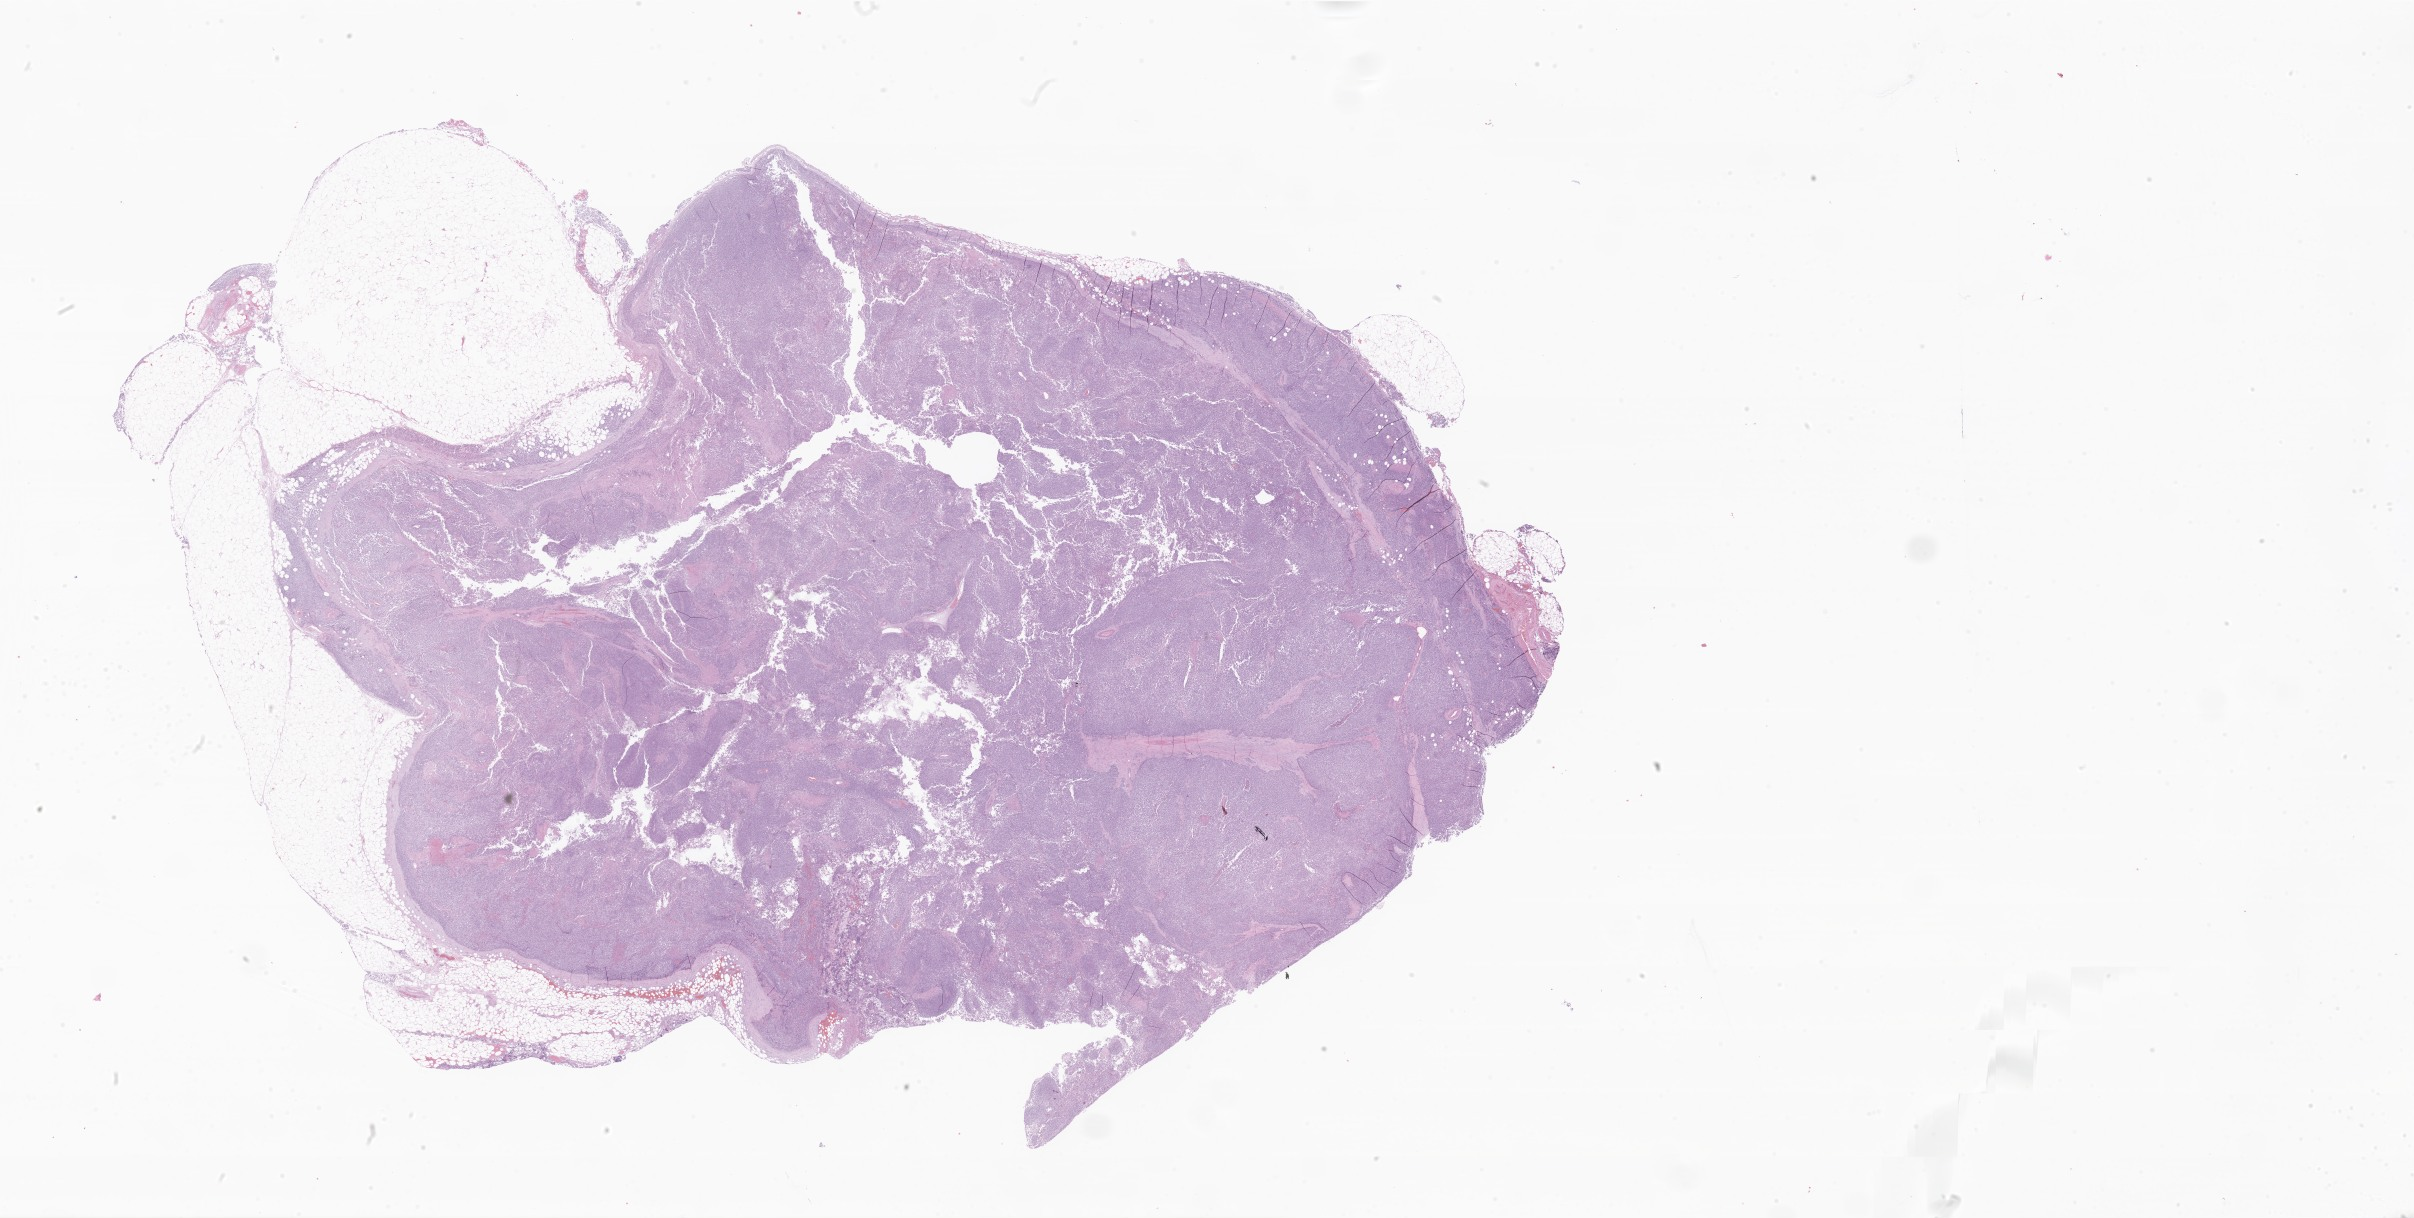
Whole-slide image, H&E stain of tumor tissue from the soft tissue of pelvis, a low-resolution overview of the entire scanned area, about 40.7 x 20.5 mm, formalin-fixed paraffin-embedded section. Patient male; age 238 months.
Tissue or organ of origin (case record): connective, subcutaneous and other soft tissues of pelvis. Diagnosis: Alveolar rhabdomyosarcoma.